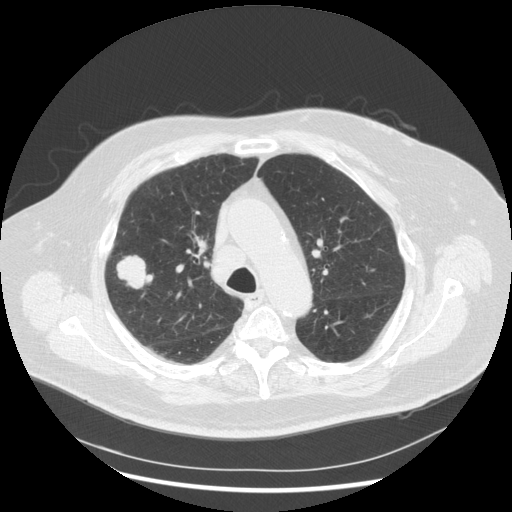
Chest CT (low-dose screening protocol), one axial image, third screening round (two years after baseline), lung window (W 1500 / L -600 HU), 2.5 mm slice thickness, slice 196 of 263 in the series, 512 × 512 image matrix, field of view 400 × 400 mm. Male participant, aged 72 years at enrolment. Former smoker at enrolment.
• Lesion marked by an expert reader, bounding box [x1, y1, x2, y2] px = [105, 251, 160, 300].
• Screening reader's record for this exam (one nodule recorded; not confirmed to be the boxed lesion): non-calcified nodule or mass ≥4 mm, right upper lobe, 31 × 31 mm, poorly defined margins, soft tissue attenuation, pre-existing on the prior screen: no.
• Official screen result: positive, other.
• Participant outcome: lung cancer diagnosed 70 days after this screen — squamous cell carcinoma, NOS, right upper lobe, poorly differentiated (G3), stage IIIA (AJCC 6th edition), 19 mm at pathology.